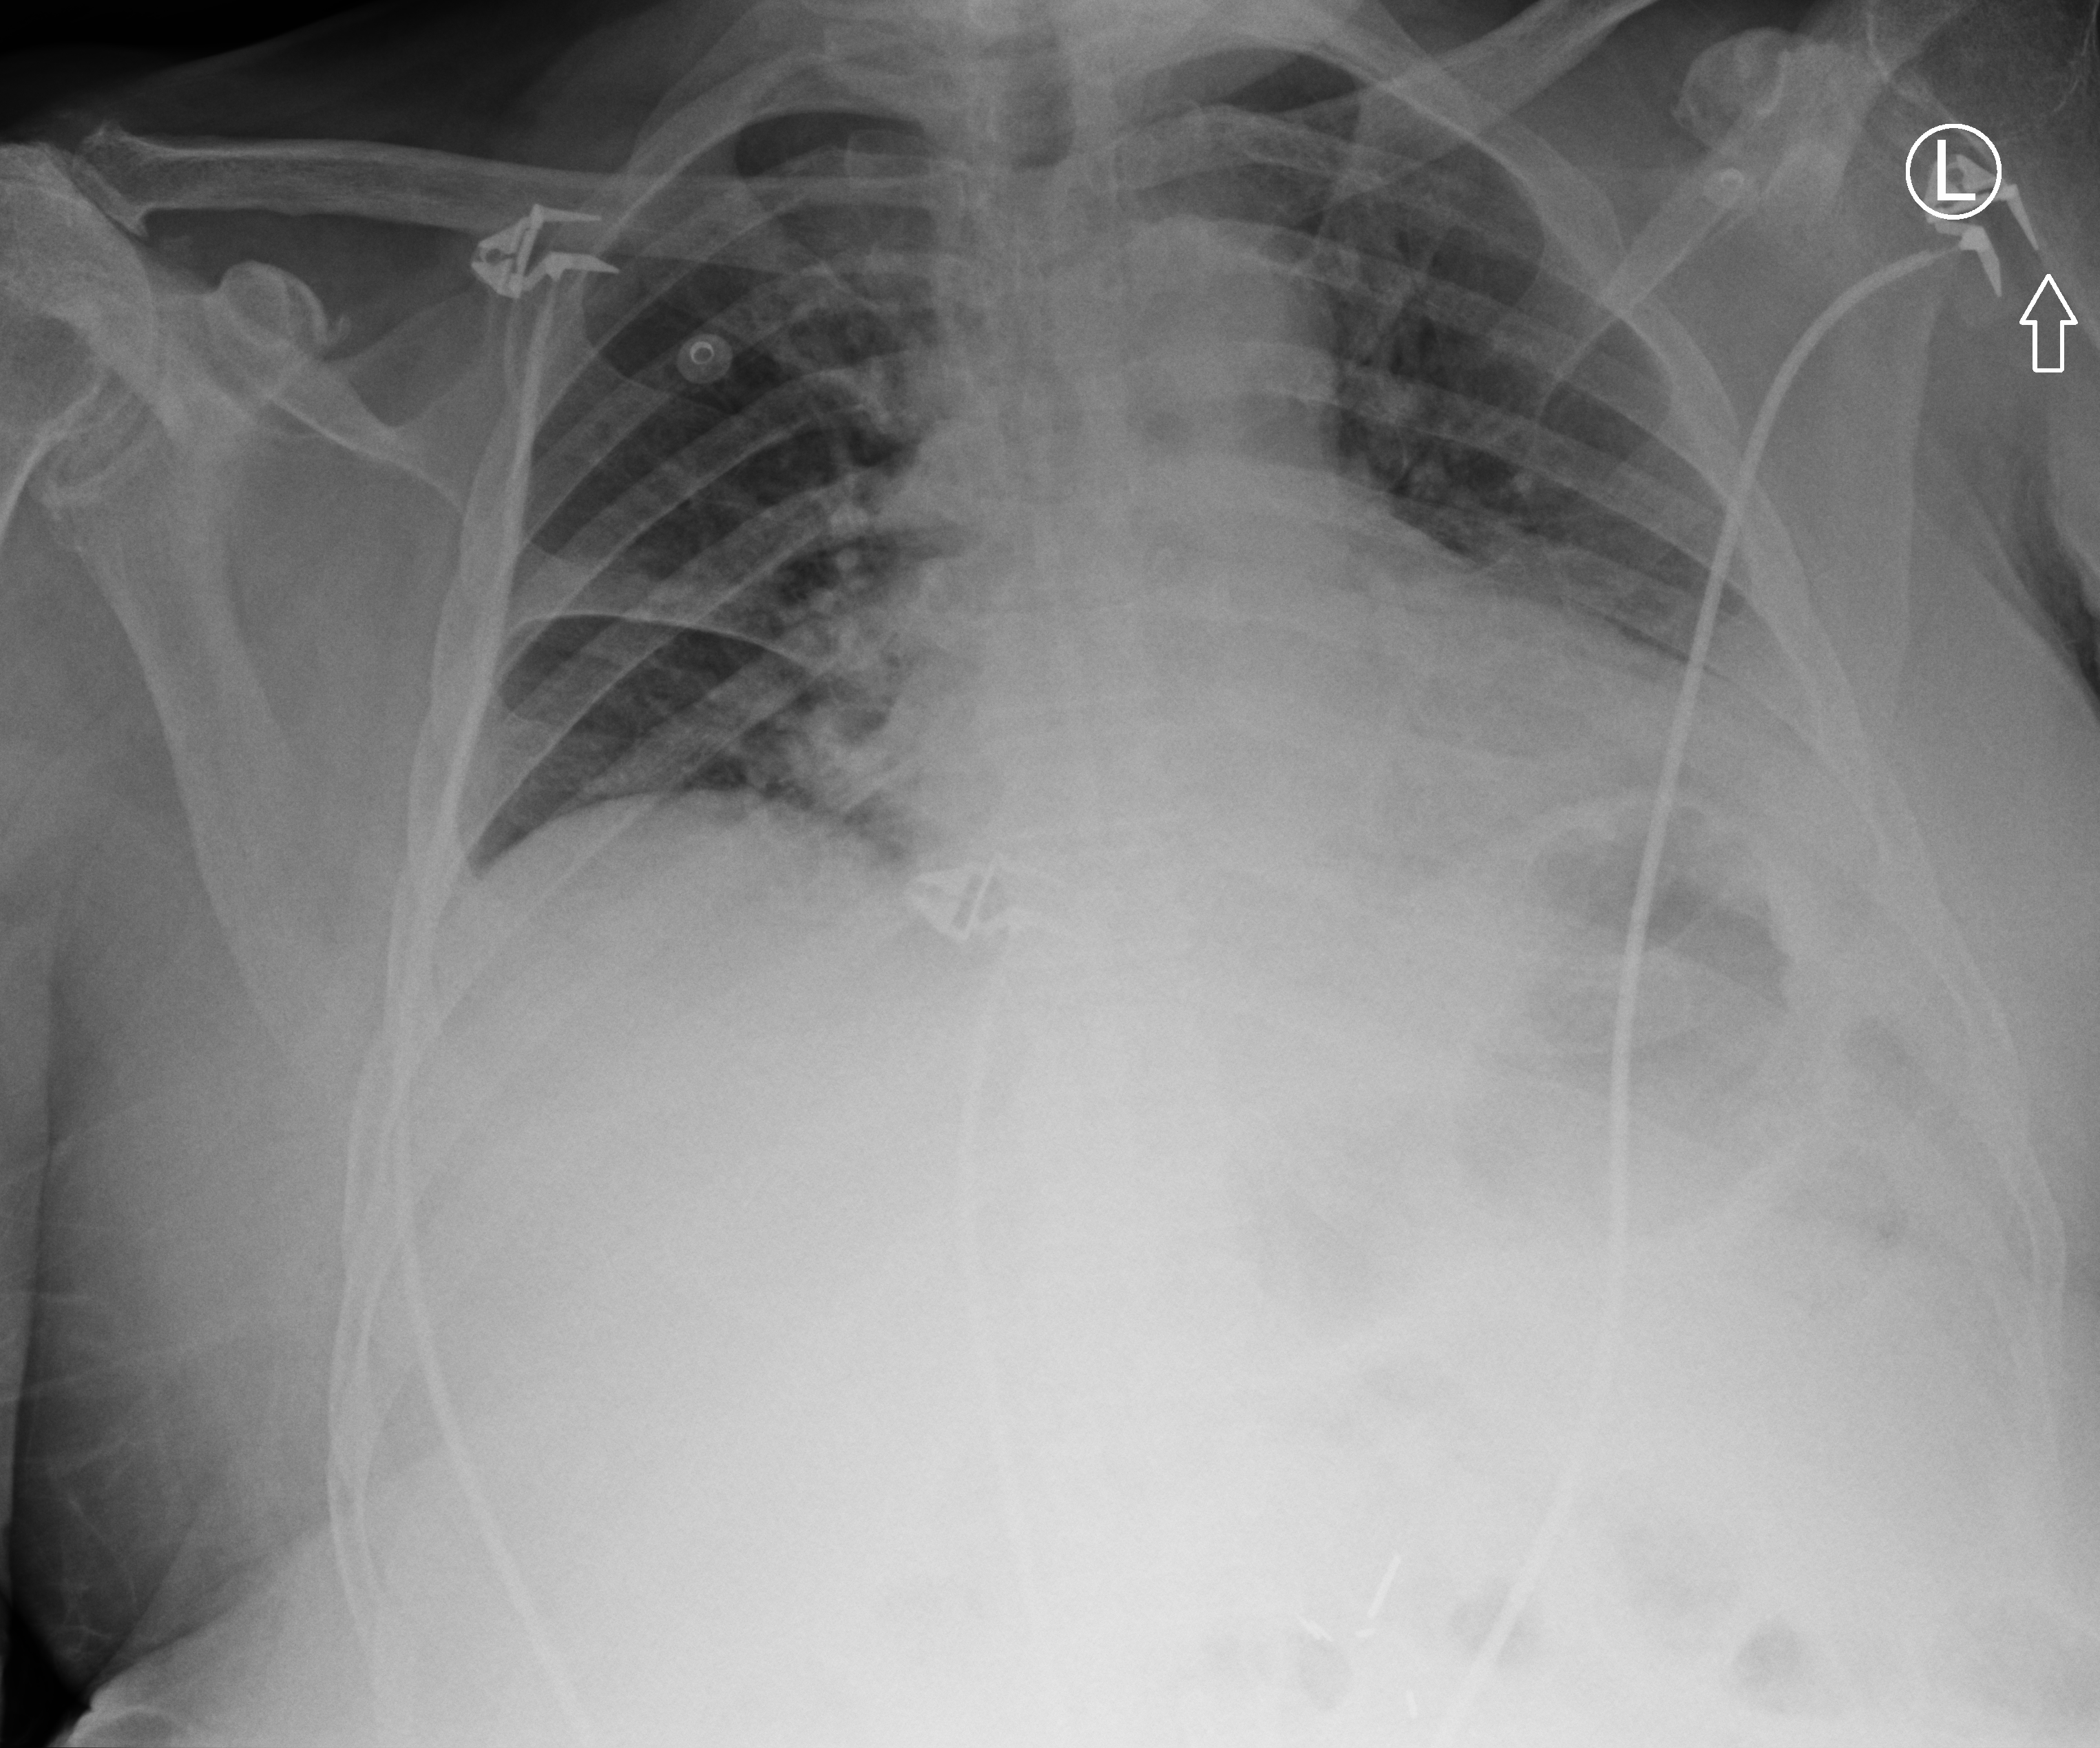
Portable chest radiograph. Male patient hospitalised with COVID-19, age 75–90 years.
Admission-level facts for this patient (not findings on this image; timing relative to this image not recorded): hypertension (admission record): yes; admitted to intensive care during this hospital stay: yes; mechanically ventilated during this hospital stay: yes.